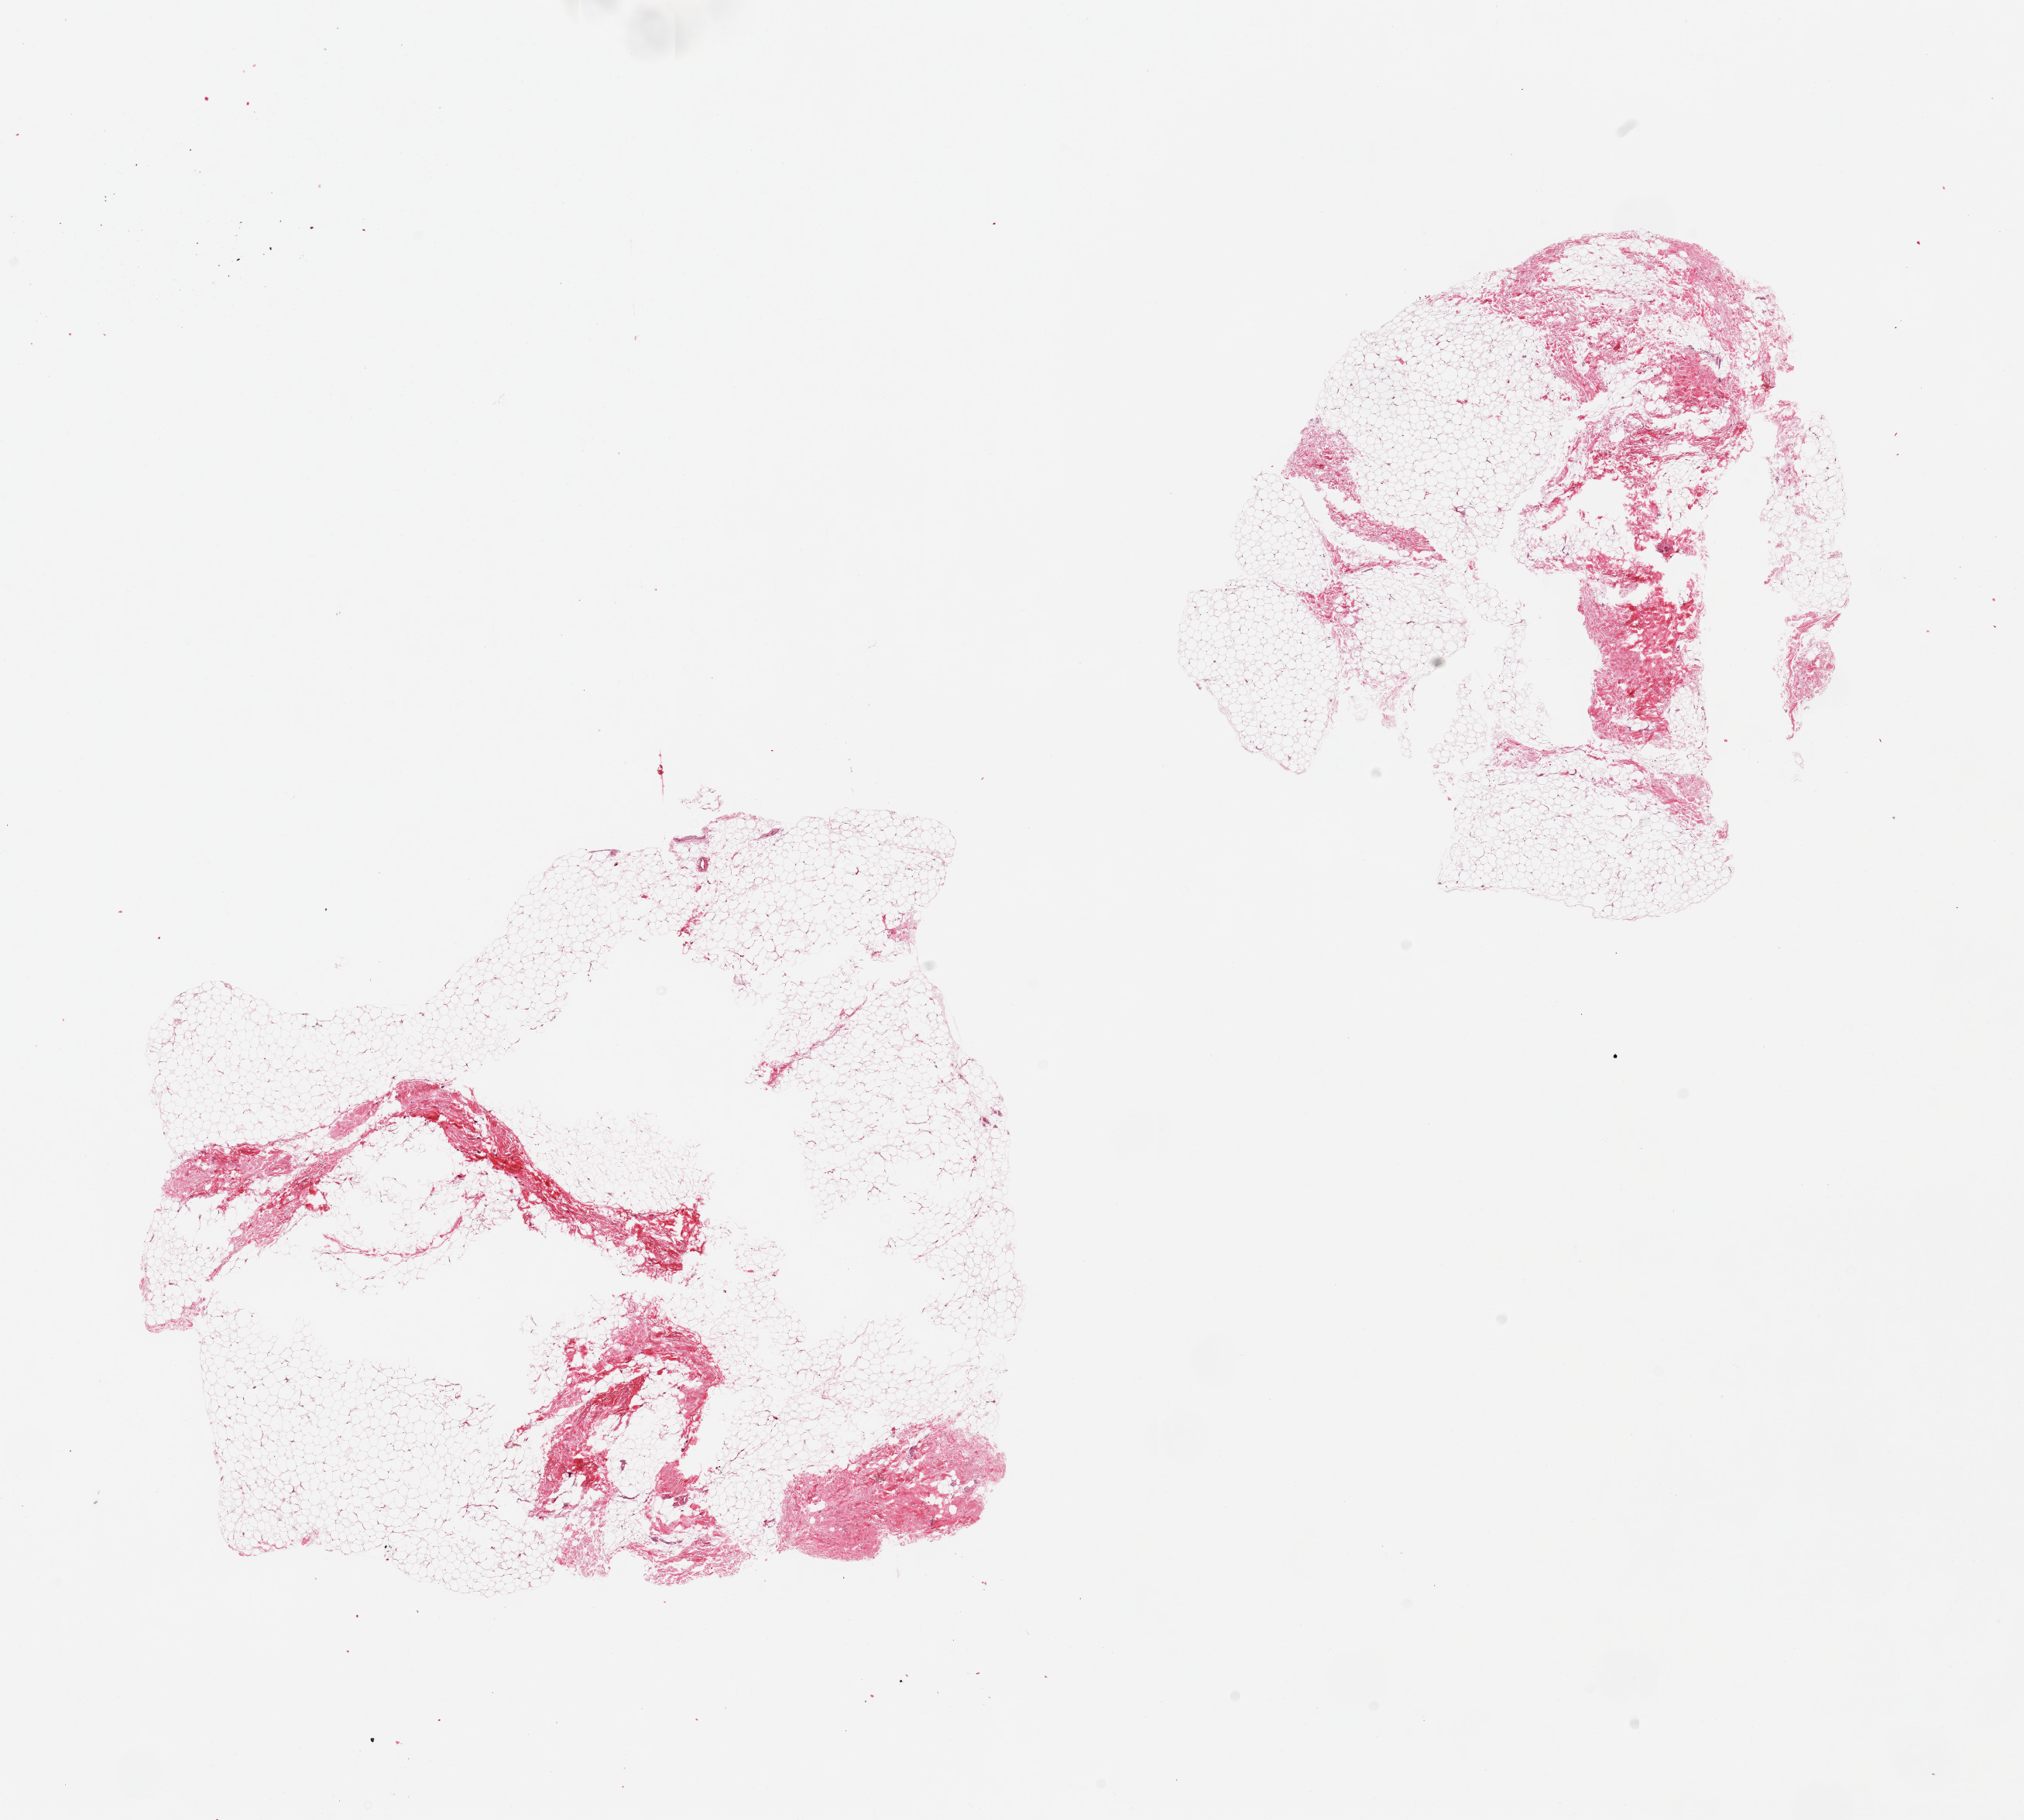
Digitized H&E-stained section, whole scanned area (about 20.7 x 18.6 mm, acquisition: 20x scan) shown as a low-resolution overview, PAXgene-fixed paraffin-embedded (PFPE) section, target tissue: breast, donor tissue sample. Male donor.
Pathologist's review note for this sample: 2 pieces; fat with 20% to 30% fibrocollagenous stroma and no evidence of ductal structures.